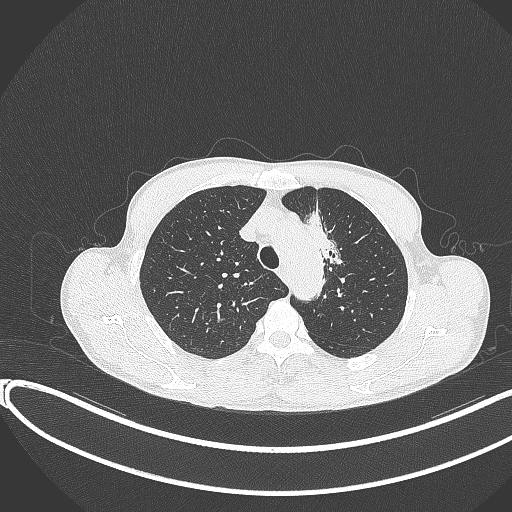
Chest CT, one axial slice; position 295 of 374 along the scan axis; reconstruction kernel B70f; lung window (W 1500 / L -600 HU); 1 mm slice thickness; 512 × 512 image matrix. Male patient, age 58 years. Case-level facts recorded for this patient, not image findings: clinical TNM (as recorded): T1c N1 M0.
Structures marked on this image (rectangle marked by the reading radiologist):
- lung tumour (recorded histology: adenocarcinoma): bounding box (x1, y1, x2, y2) in pixels: (301, 201, 342, 272)